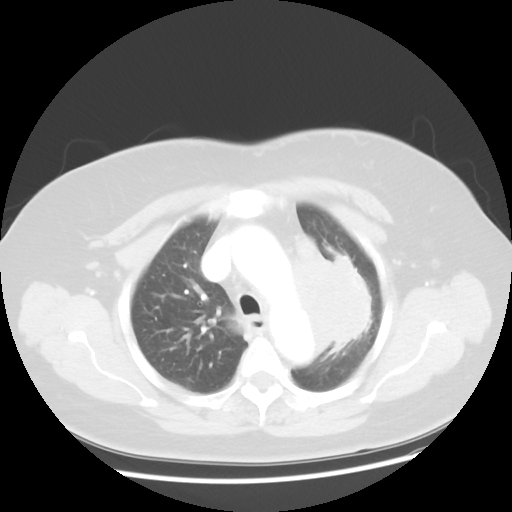
Chest CT, one axial slice; position 35 of 49 along the scan axis; reconstruction kernel STANDARD; 120 kVp; lung window (W 1500 / L -600 HU); 5 mm slice thickness; 512 × 512 image matrix, field of view 374 × 374 mm. Patient: female, 58 years. From the clinical record (not read from this slice): clinical TNM (as recorded): T4 N3 M0; histopathological grade: G3.
Outlined on this slice (rectangle marked by the reading radiologist):
- lung tumour (recorded histology: small cell carcinoma): bounding box [x1, y1, x2, y2] px = [284, 227, 387, 357]